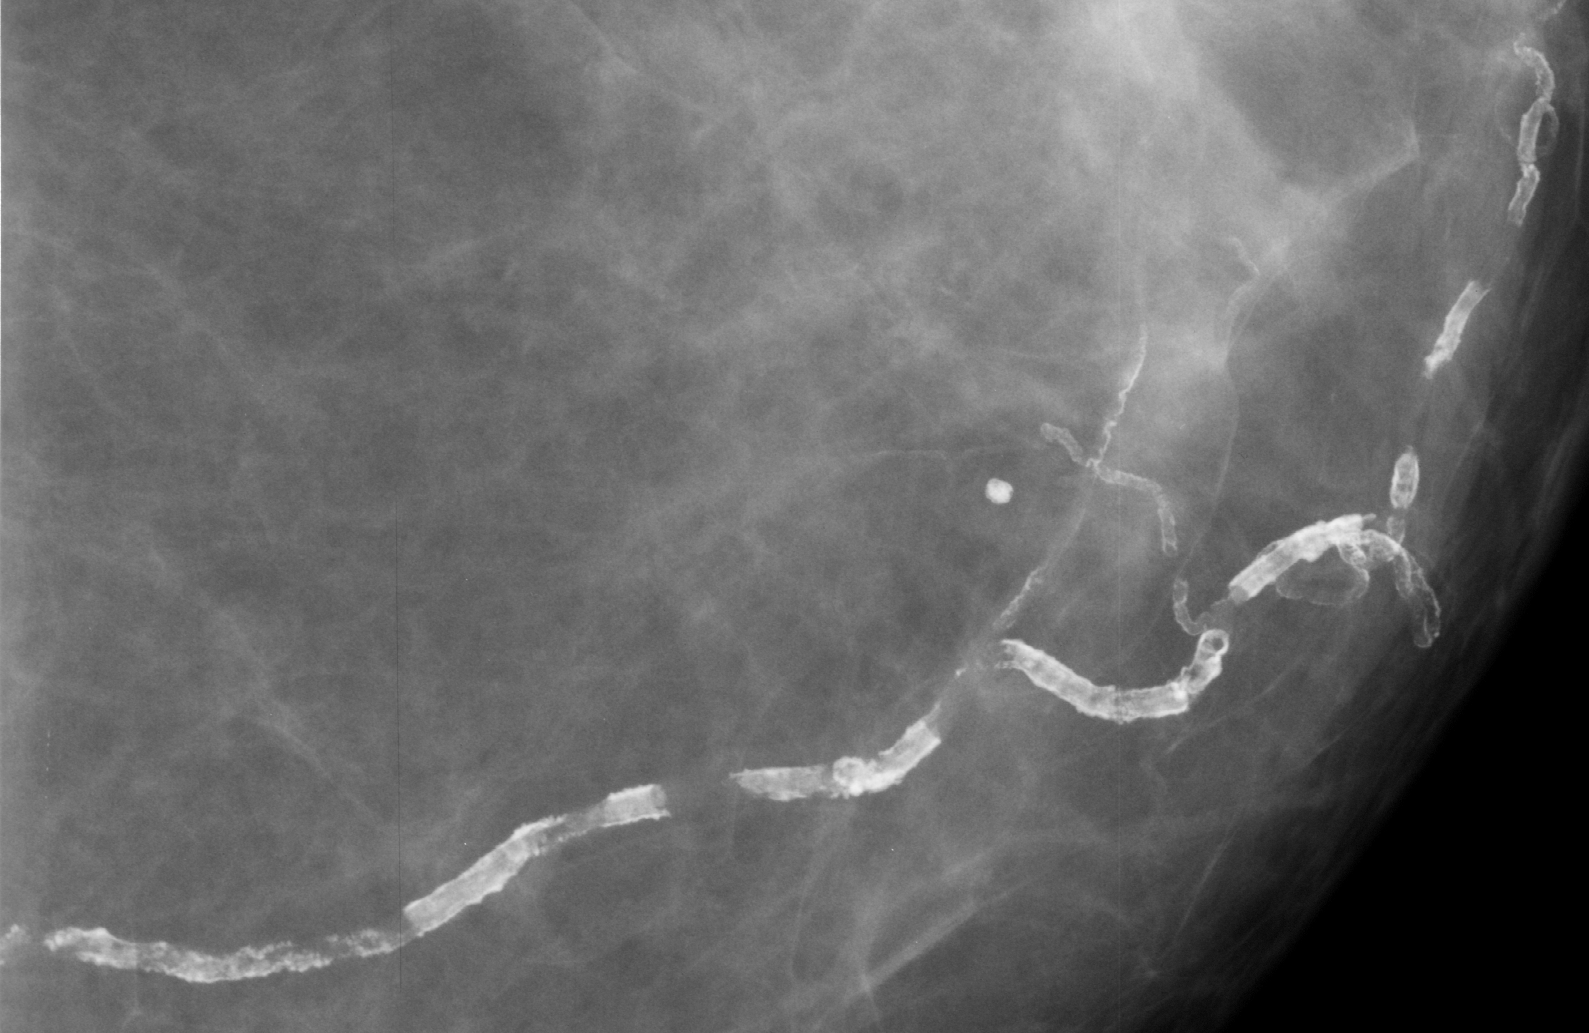
Region of interest cut from a scanned film mammogram (one marked finding); left breast; CC view; BI-RADS breast density category 2 (scale 1–4).
Finding: calcifications, morphology vascular; BI-RADS assessment category 2; benign without callback (not worked up further).